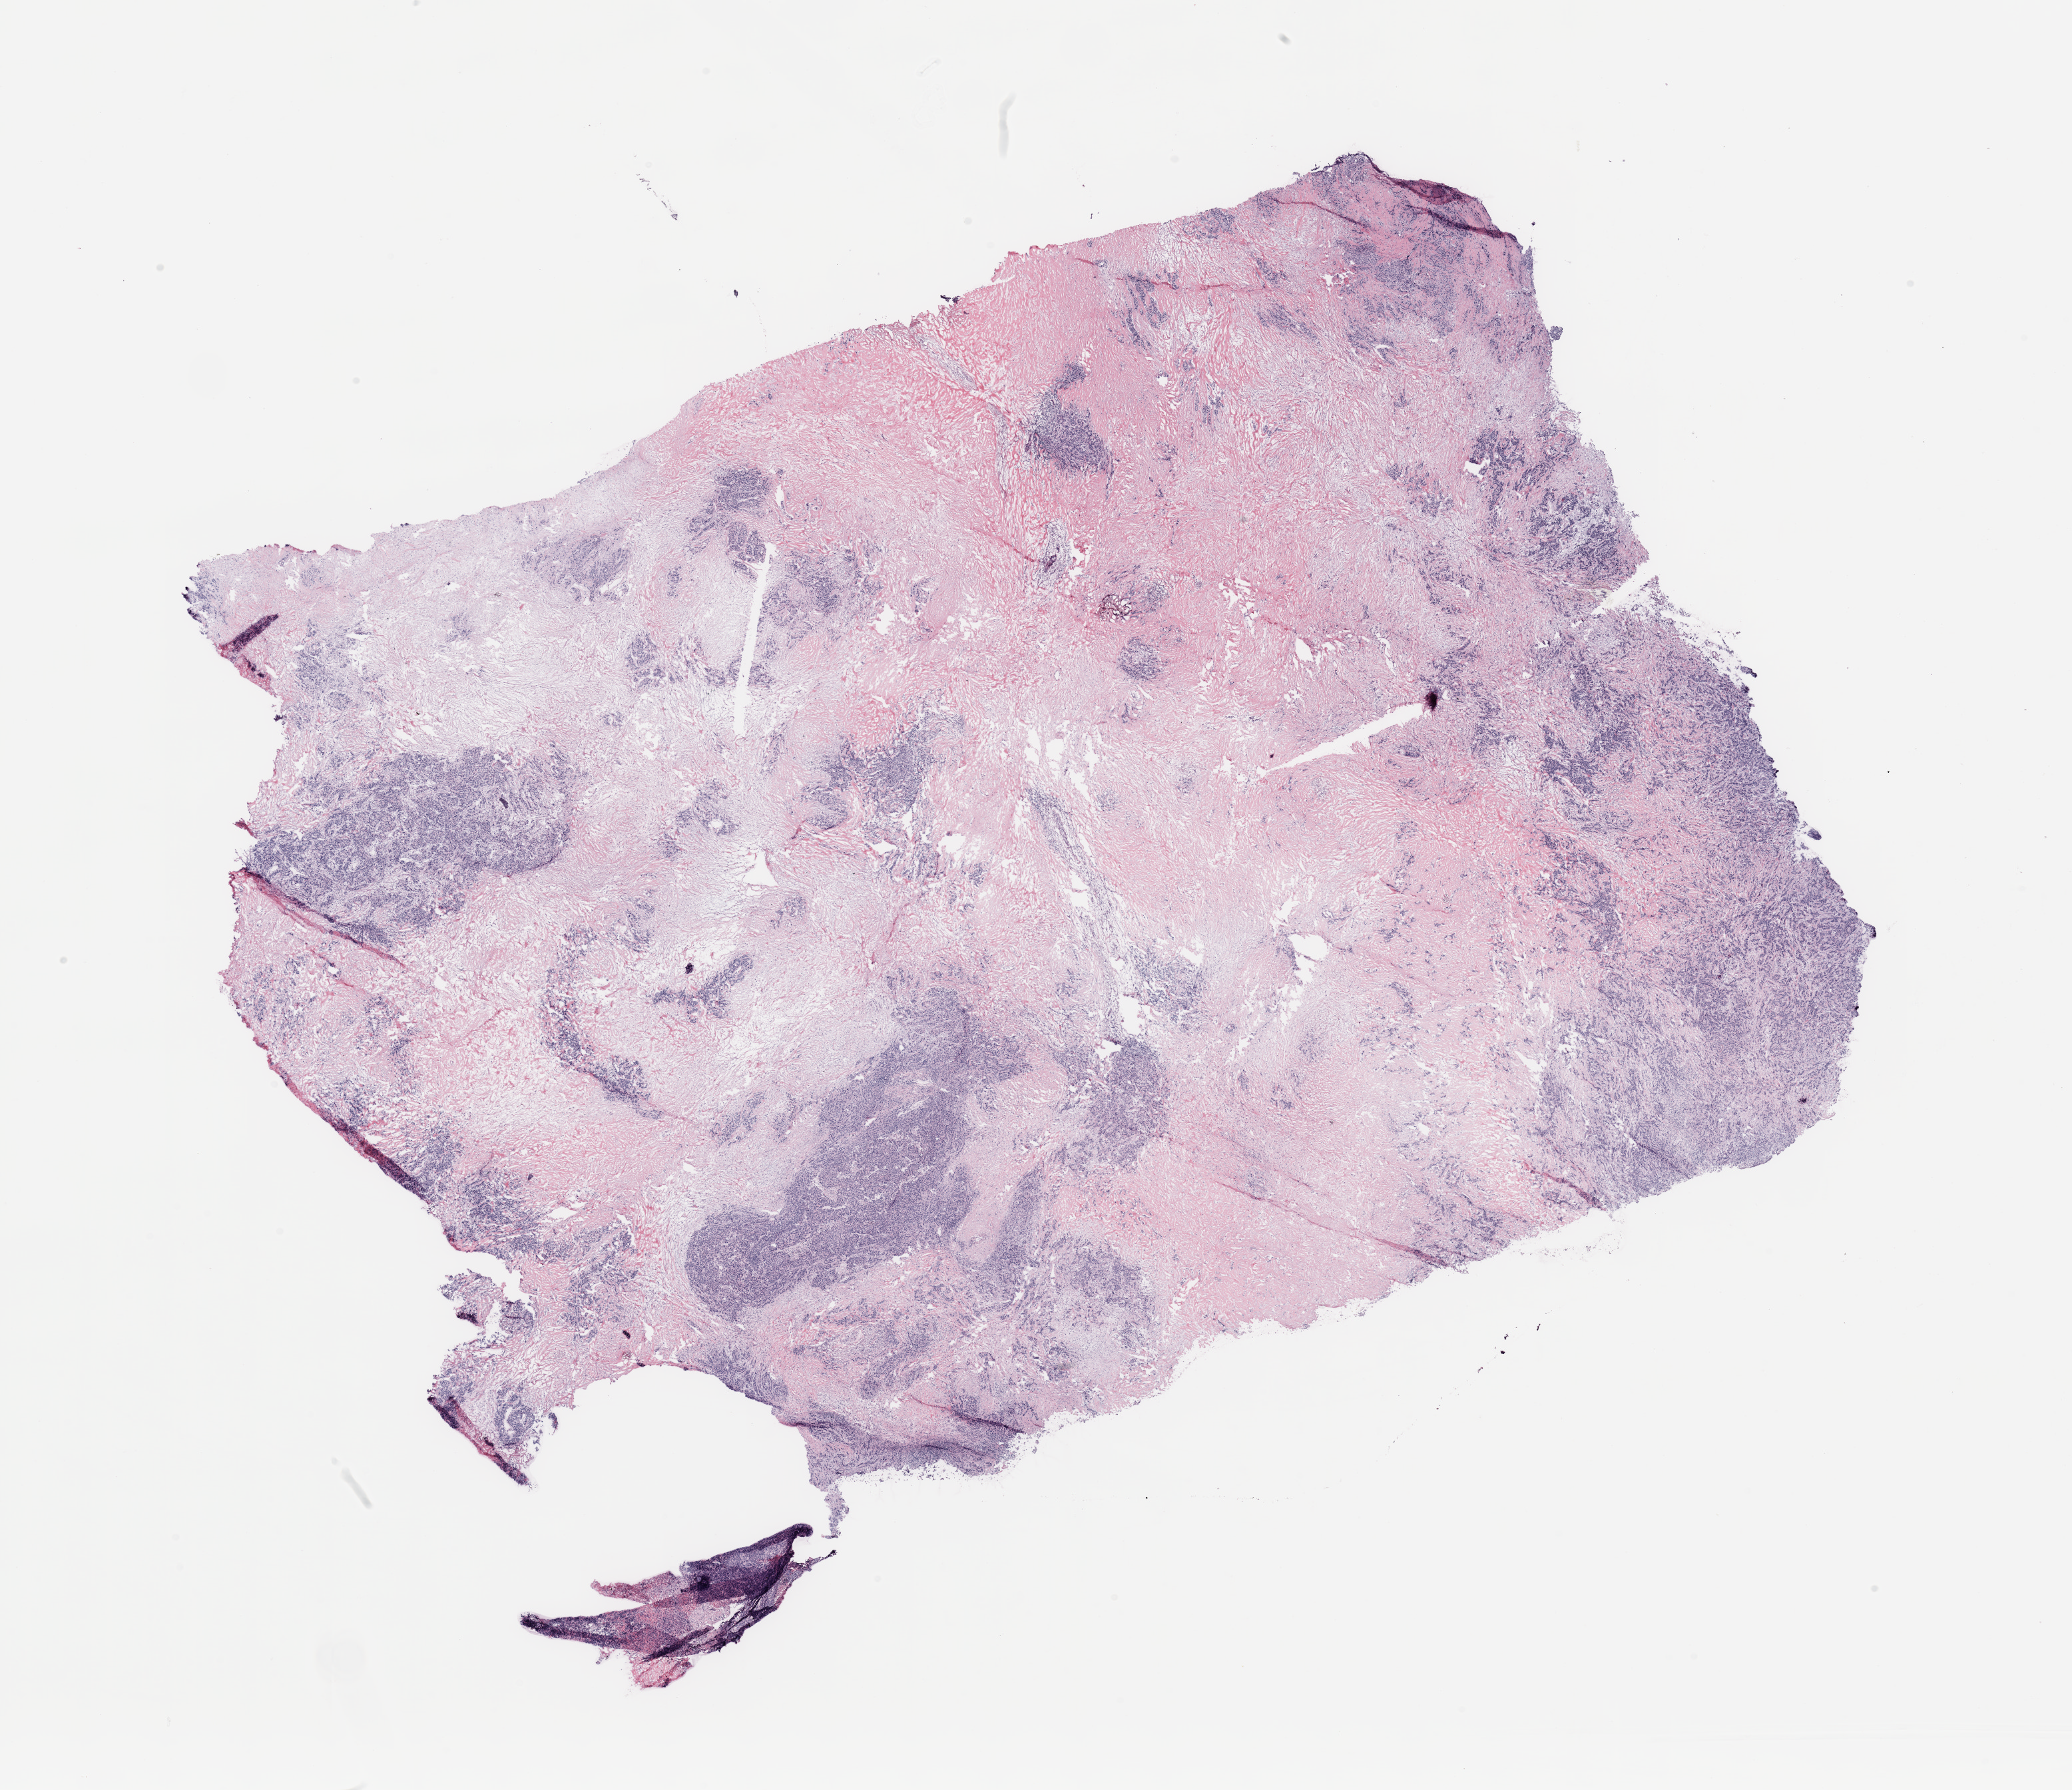
H&E whole-slide image — whole scanned area (about 24.6 x 21.3 mm) shown as a low-resolution overview. Breast, tissue type not recorded.
Patient diagnosis (cohort enrolment): breast cancer (breast).